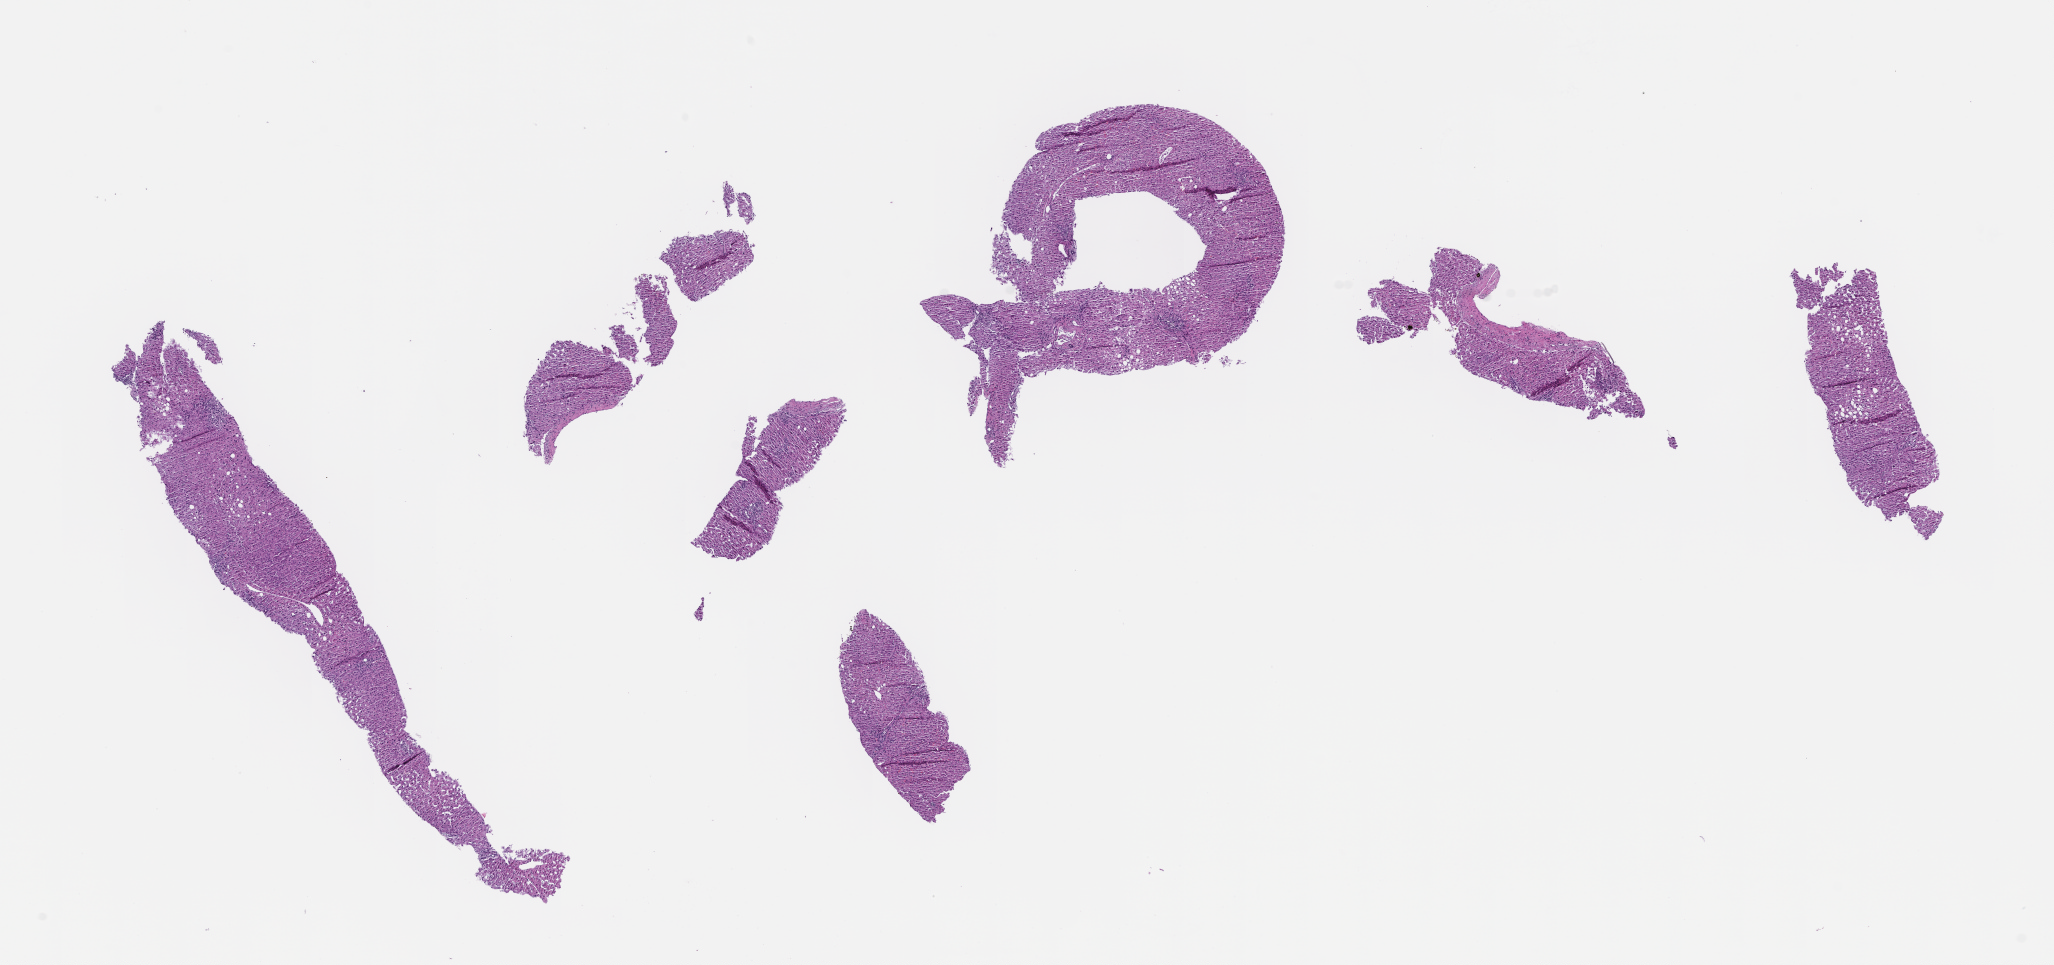
Haematoxylin and eosin whole-slide image — whole scanned area (about 16.6 x 7.8 mm) shown as a low-resolution overview; formalin-fixed, paraffin-embedded (FFPE) tissue; specimen time point: collected at baseline (before treatment). Patient sex: male.
• this section: metastatic tumor tissue
• patient diagnosis (primary): Colorectal Carcinoma